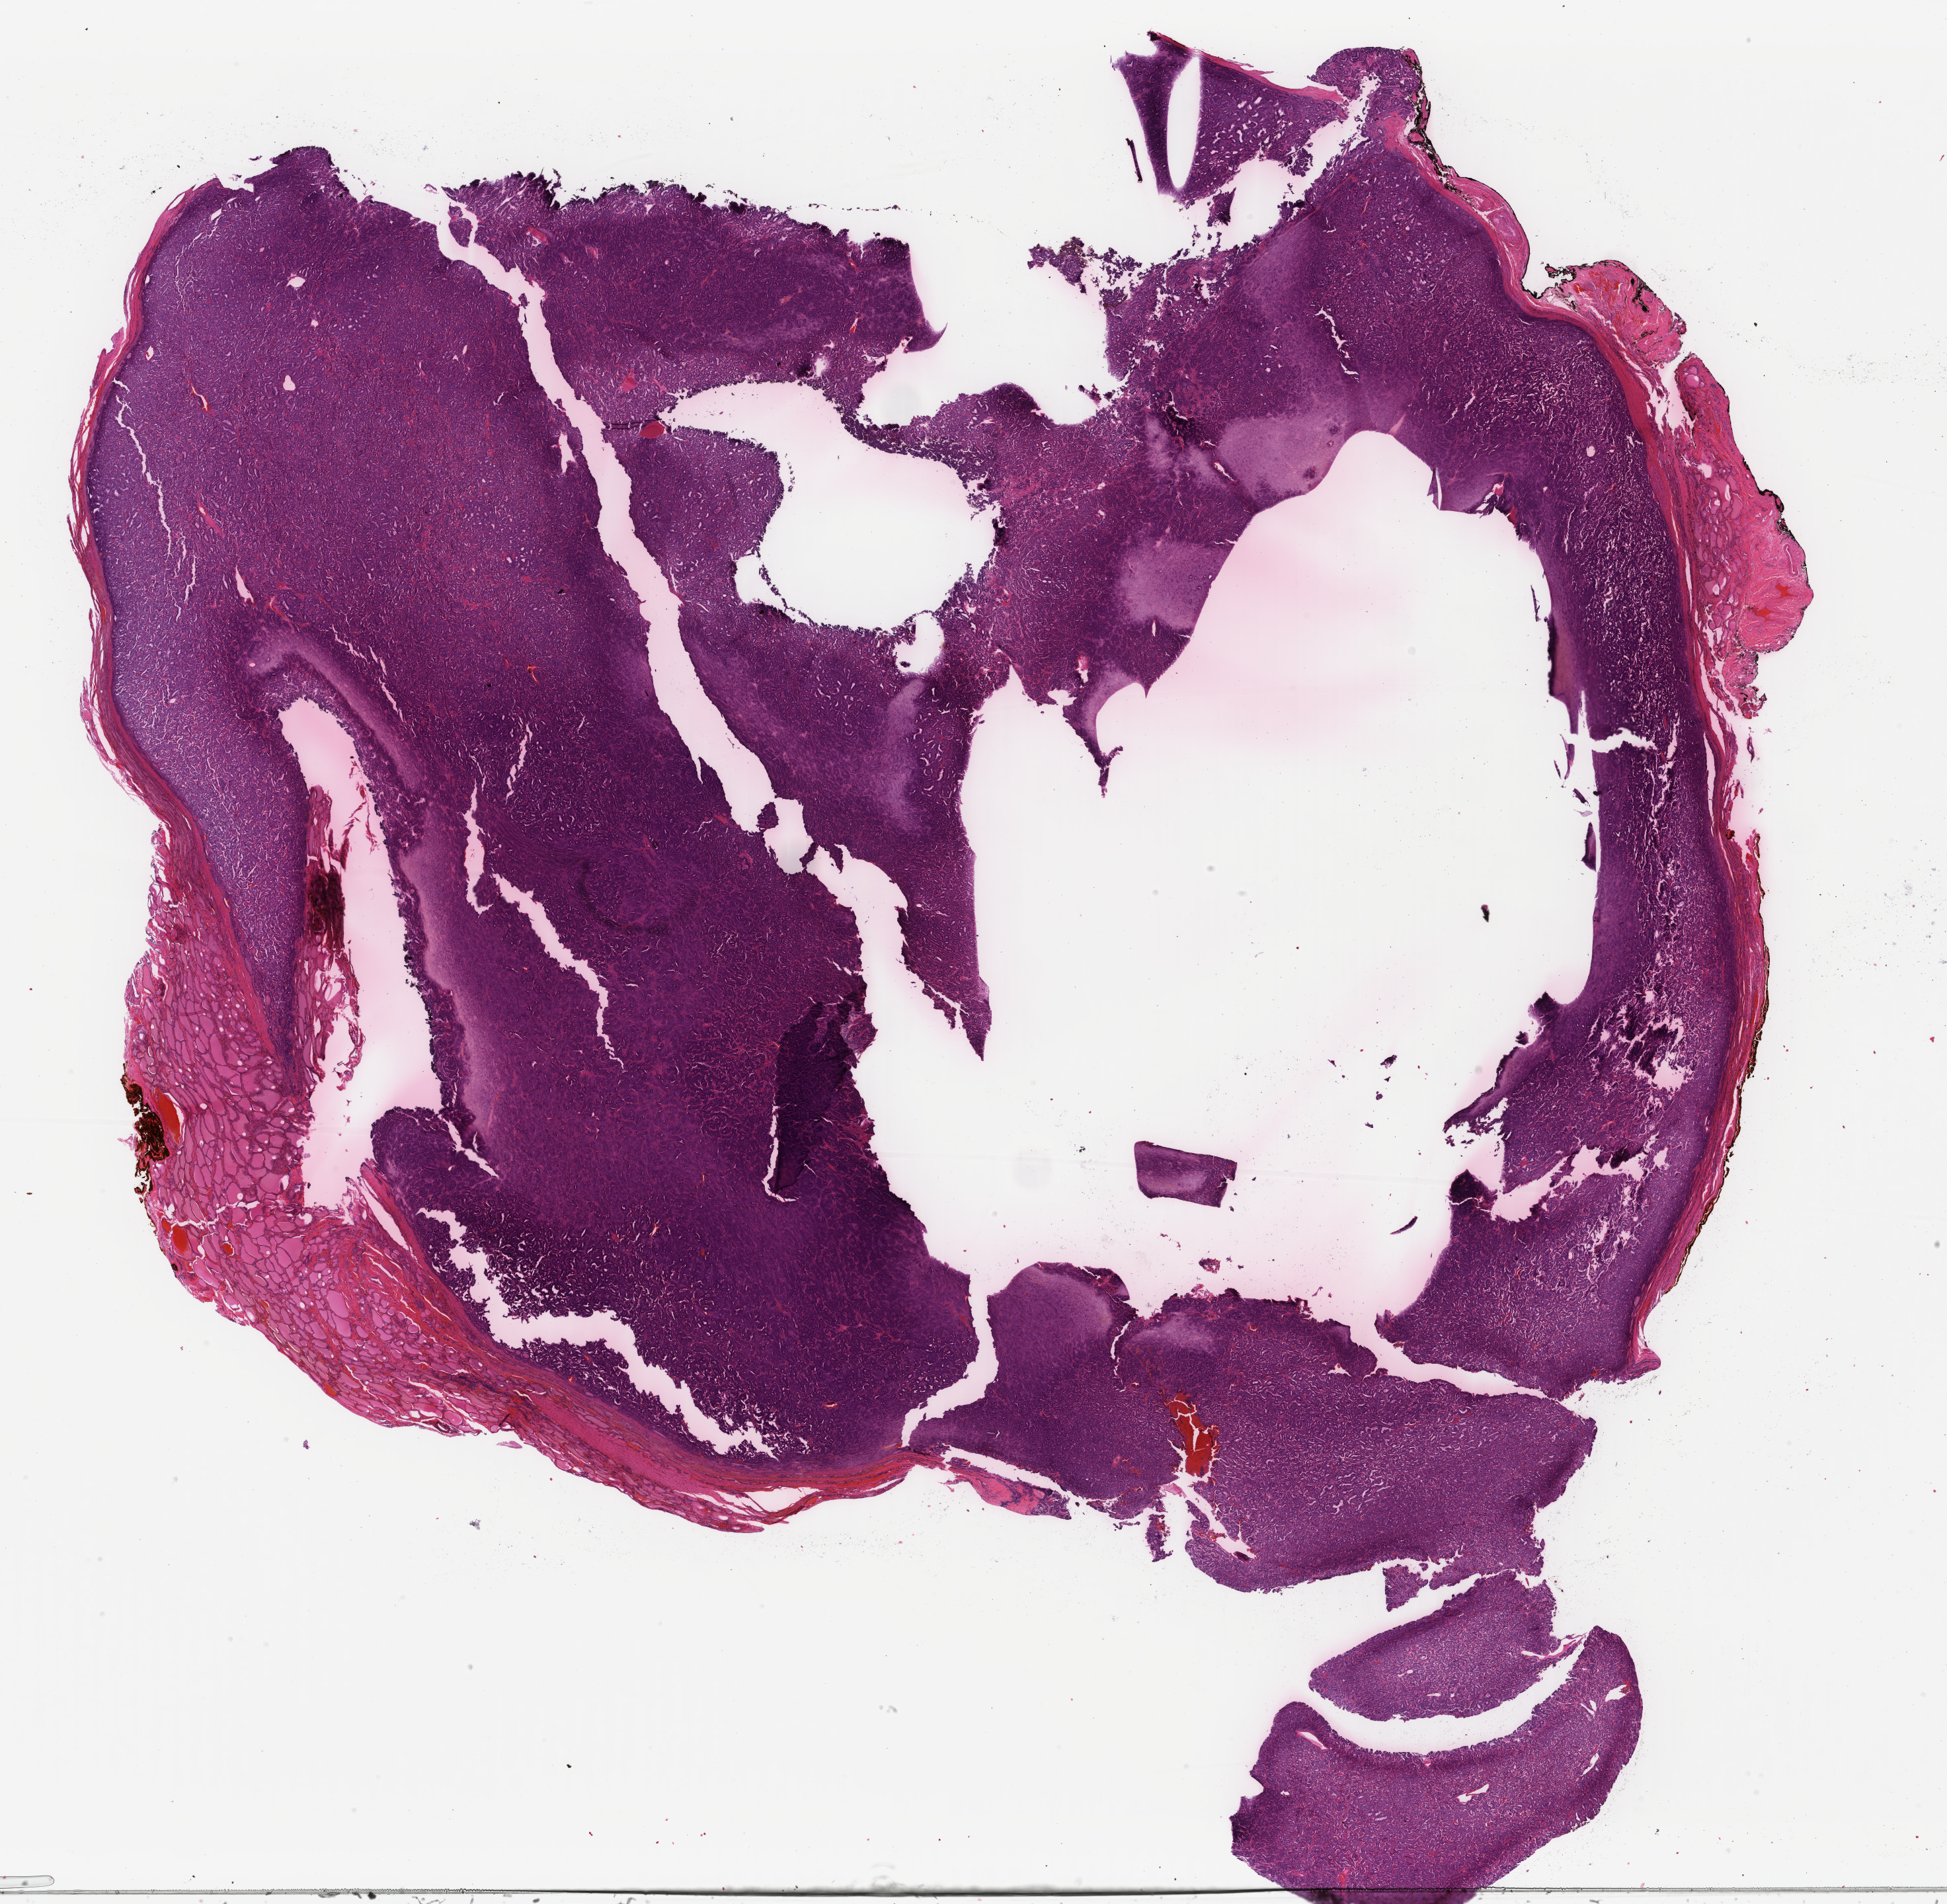
H&E-stained whole-slide image — low-resolution overview of the scanned area, about 23.4 x 22.9 mm (acquisition: 40x scan), FFPE section, sample: primary tumour, thyroid. Female, age 30 years at initial diagnosis.
AJCC pathologic stage: I (7th edition). Diagnosis: Papillary adenocarcinoma, NOS (thyroid gland).